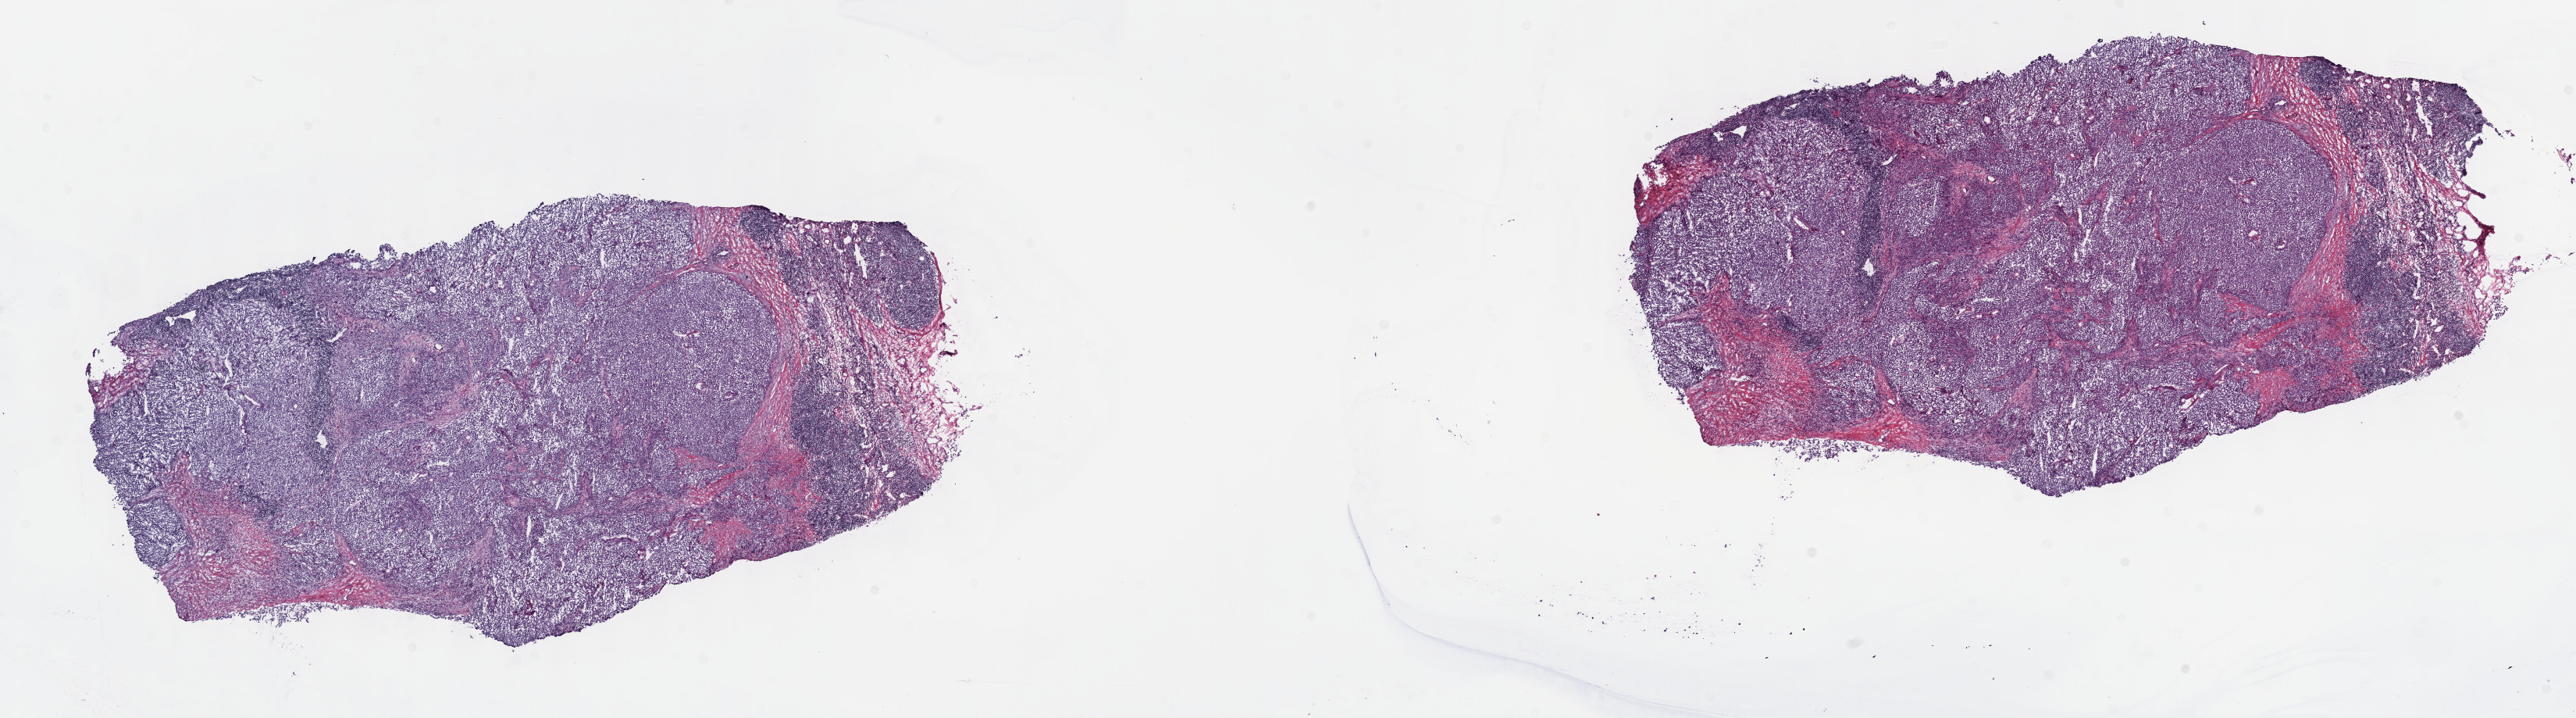
H&E-stained whole-slide image — shown as a low-resolution overview of the whole scanned area (about 26.7 x 7.4 mm); frozen section from the top of the tissue portion; metastatic tumour sample, sampled site: lymph nodes of axilla or arm. Patient: male, age at initial diagnosis 41 years. Slide review estimates, as recorded: tumour cells 60%, tumour nuclei 80%, normal cells 20%, stromal cells 20%, necrosis 0%. Inflammatory infiltration, as recorded: lymphocyte infiltration 90%, monocyte infiltration 10%, neutrophil infiltration 0%.
* this section: metastatic tumour tissue
* patient diagnosis: Malignant melanoma, NOS